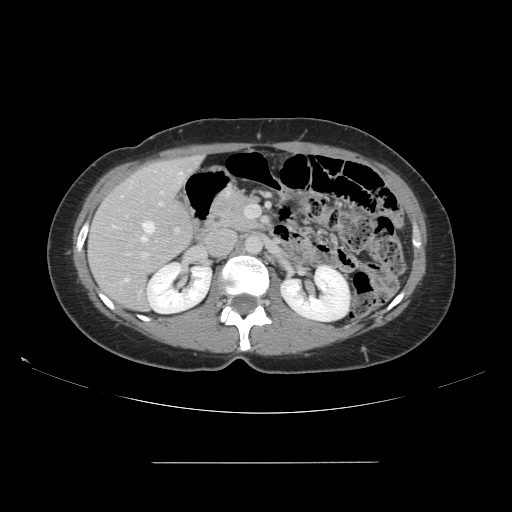
Contrast-enhanced abdominal CT, one axial slice. Slice 79 of 151 in the series (ordered by position). 120 kVp. Intravenous contrast given. Soft-tissue window (W 400 / L 40 HU). 512 × 512 image matrix, field of view 421 × 421 mm. Female patient, age 46 years. Case-level facts recorded for this patient, not image findings: diagnosis: colorectal cancer liver metastases, imaged before liver resection; multiple liver metastases: yes; largest metastasis: 3 cm; disease in both lobes: yes.
Annotated regions visible in this slice (manually delineated by an expert):
- hepatic veins: bounding box [x1, y1, x2, y2] px = [113, 195, 155, 281]
- liver: [89, 157, 200, 311]
- planned liver remnant (the part of the liver to remain after resection): [97, 157, 199, 312]
- portal vein (with intrahepatic branches): [124, 190, 246, 260]